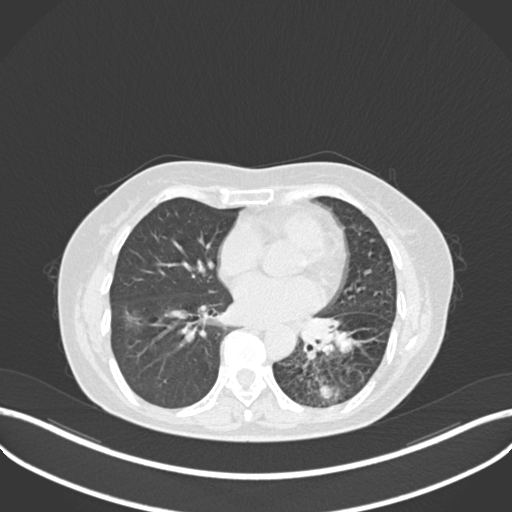
Chest CT, one axial slice. Position 113 of 270 along the scan axis. Reconstruction kernel B30f. 120 kVp. Lung window (W 1500 / L -600 HU). 512 × 512 image matrix. Patient: female, 63 years. From the clinical record (not read from this slice): clinical TNM (as recorded): T1b N0 M0; histopathological grade: G2-3.
Structures marked on this image (bounding box drawn by a radiologist):
- lung tumour (recorded histology: adenocarcinoma): bounding box [x1, y1, x2, y2] px = [299, 313, 359, 364]